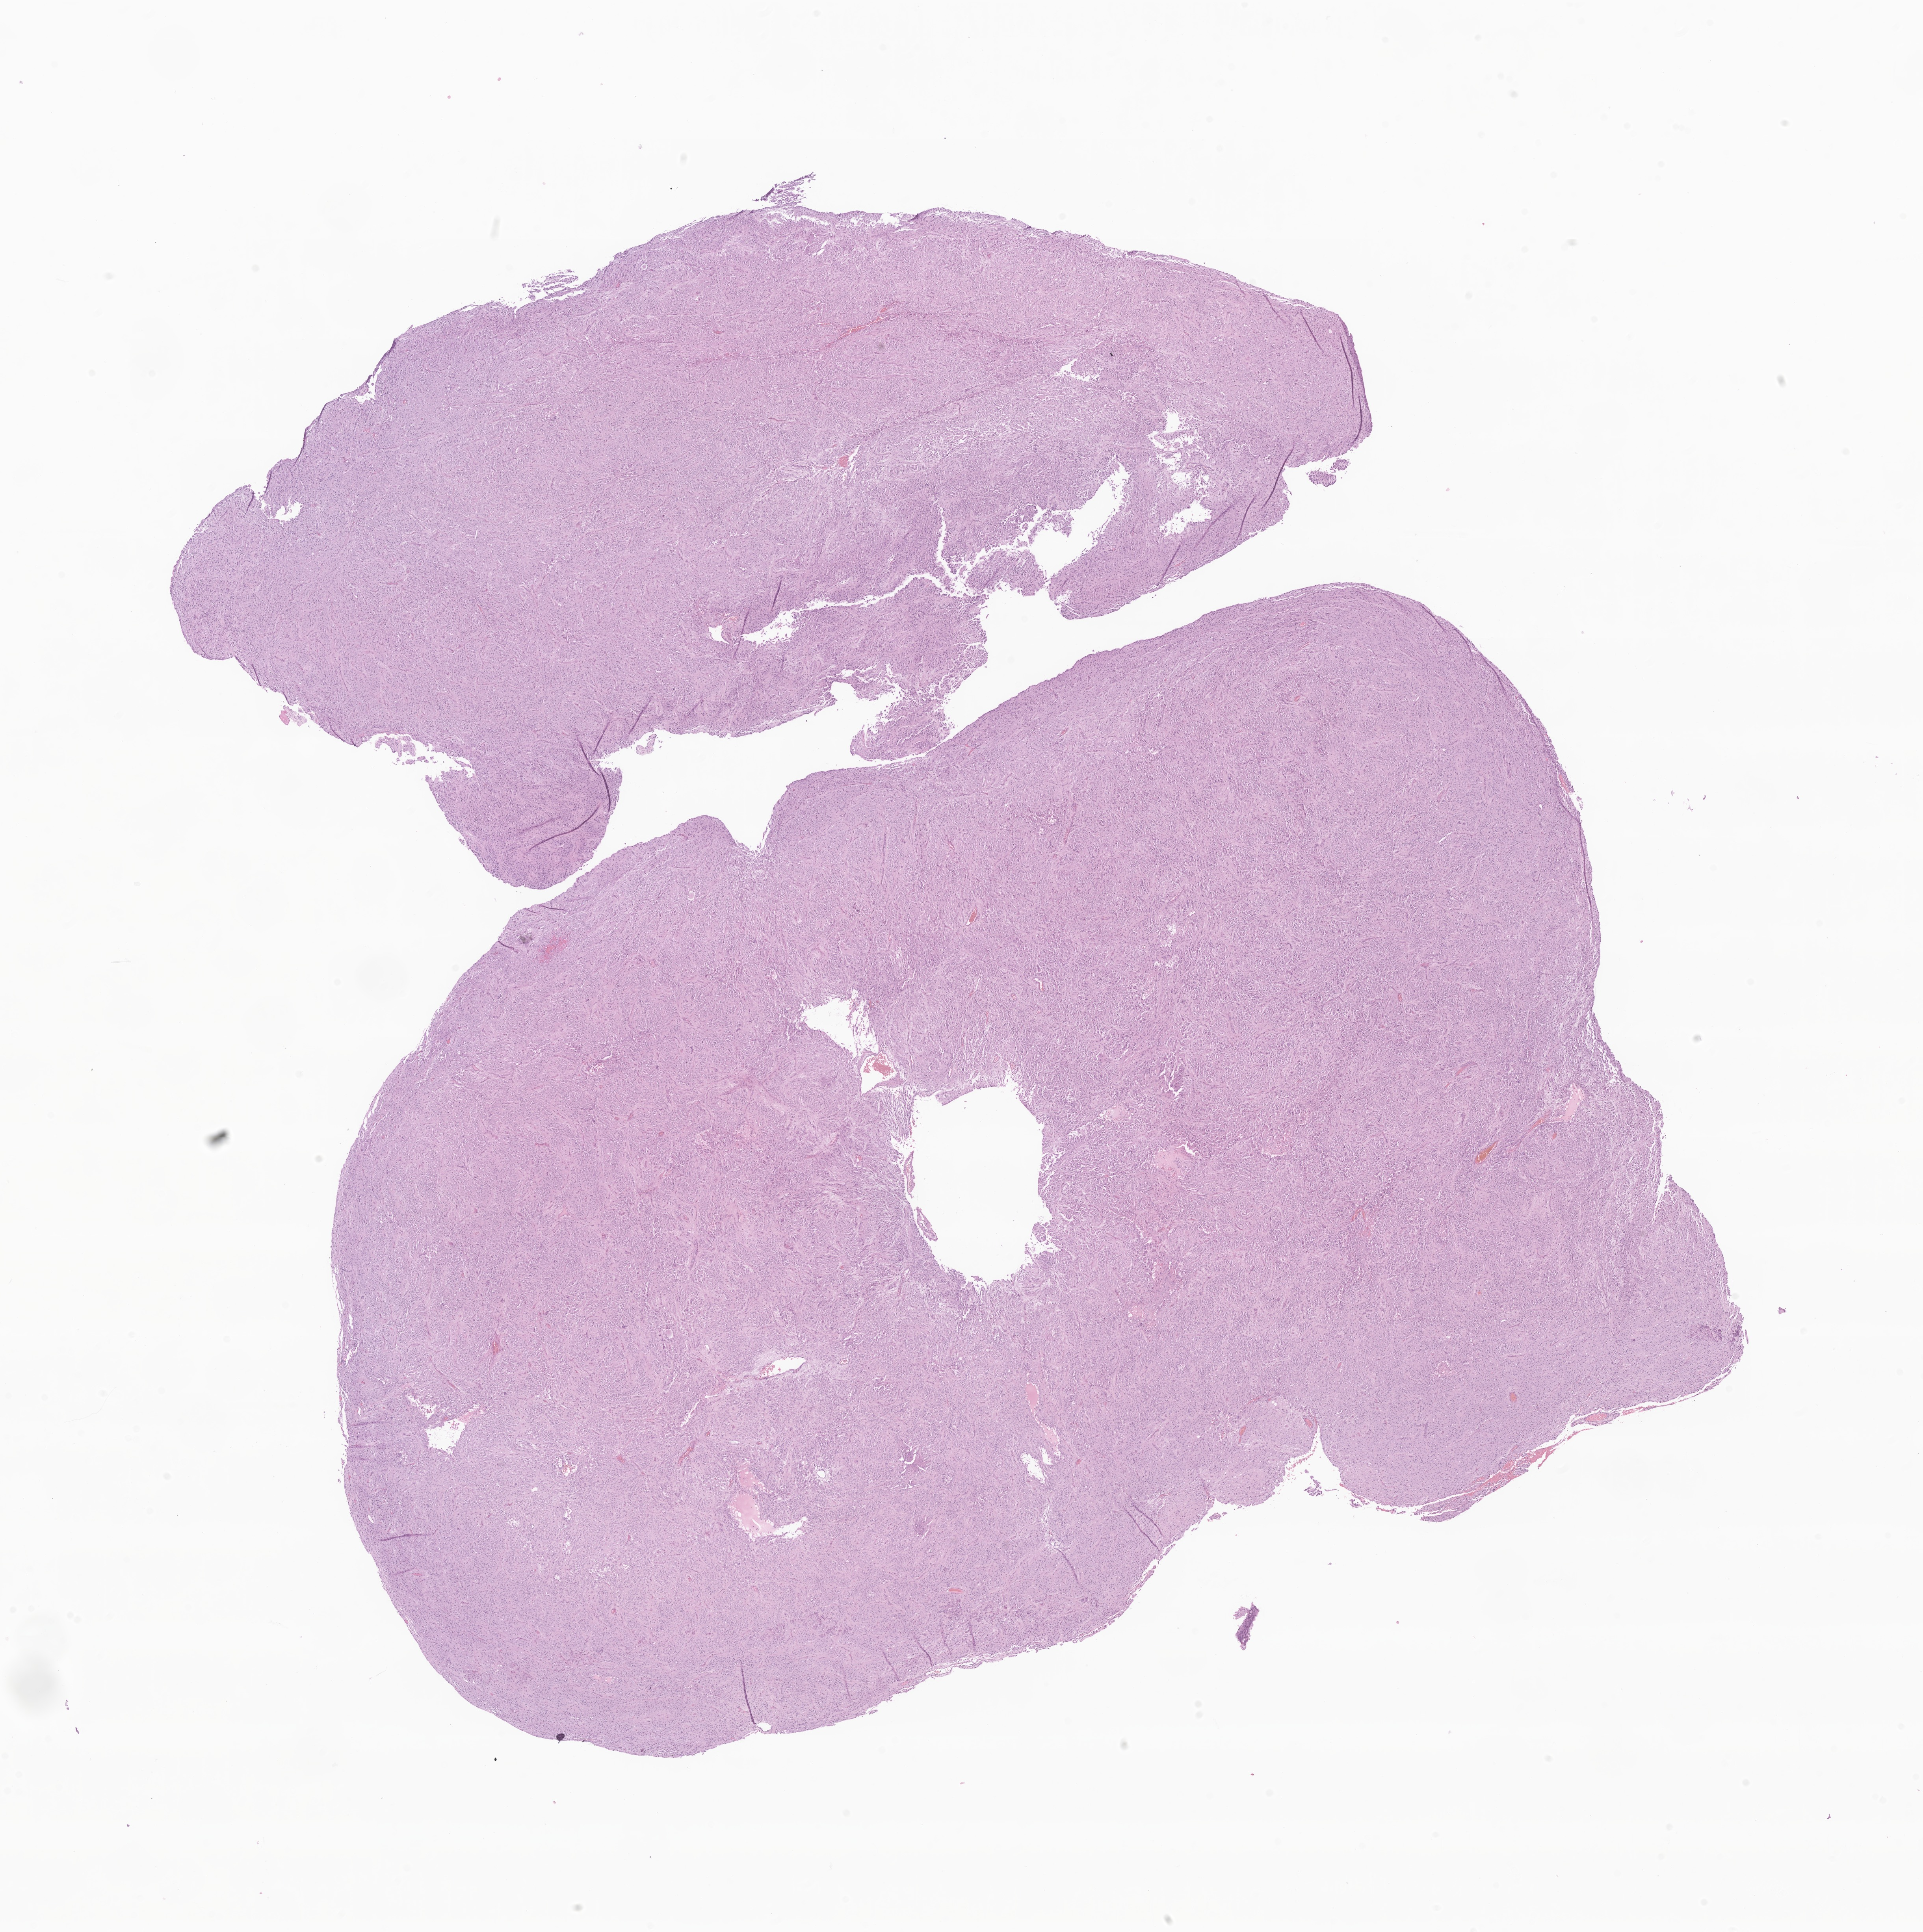
Whole-slide image, haematoxylin and eosin stain of tumor tissue from the cerebral ventricle, whole scanned area (about 20.6 x 20.7 mm) shown as a low-resolution overview. FFPE section. Patient female; age 149 months (12 years 5 months).
- diagnosis (ICD-O-3 morphology term): Subependymal giant cell astrocytoma